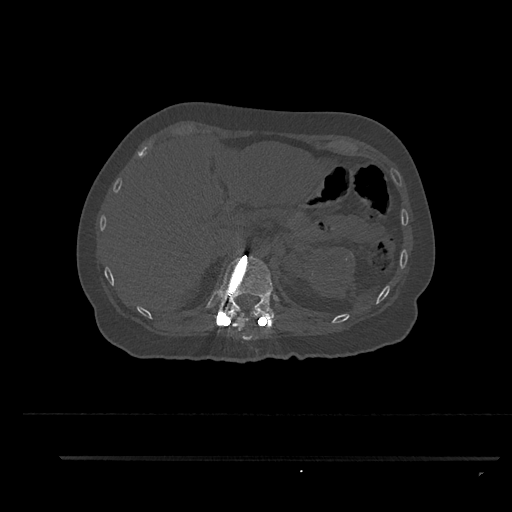
CT including the spine, one axial slice; slice 281 of 797 in the series (ordered by position); 120 kVp; bone window (W 1800 / L 400 HU); 512 × 512 image matrix, field of view 408 × 408 mm. Patient: female, 44 years. Case-level facts recorded for this patient, not image findings: primary cancer: renal; vertebrae with lytic lesions (as recorded): L1.
Structures marked on this image (semi-automatic segmentation, software-assisted and operator-edited):
- T11 vertebra: bounding box (x1, y1, x2, y2) in pixels: (232, 311, 255, 340)
- T12 vertebra: (218, 249, 282, 327)